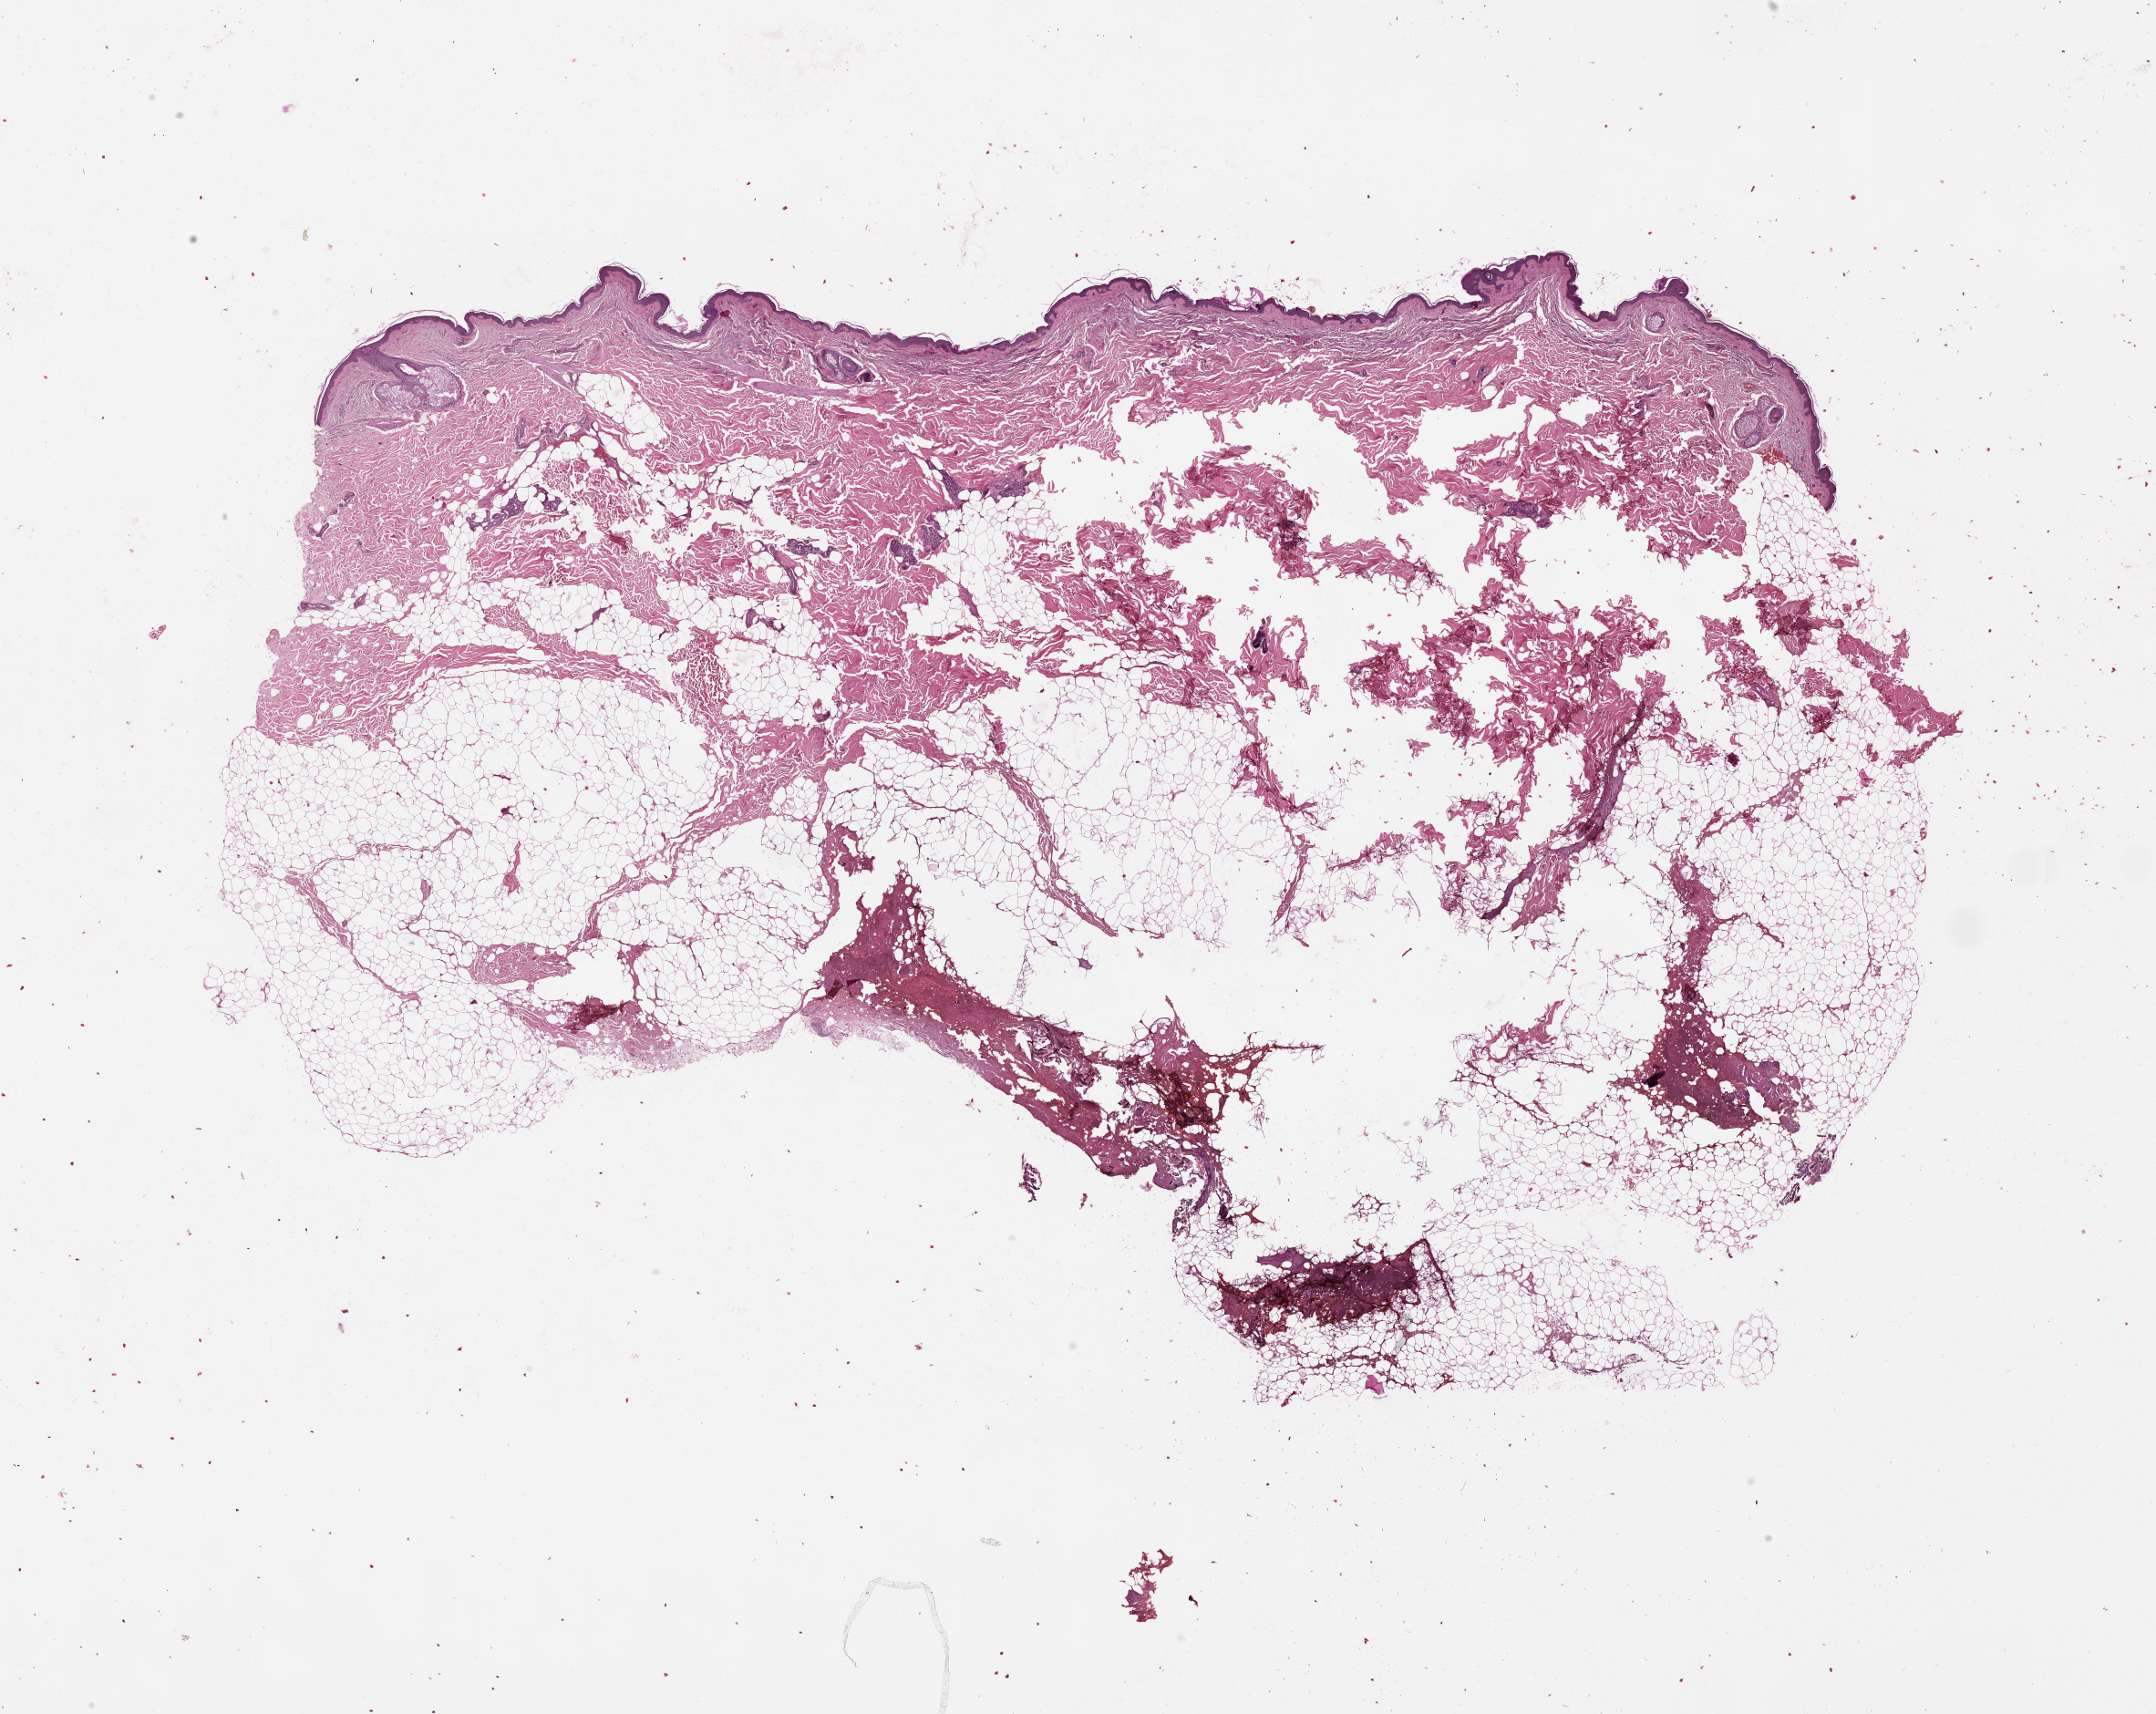
Whole-slide histology image, H&E-stained, shown as a low-resolution overview of the whole scanned area (about 19.0 x 15.1 mm). Female, 68 y/o.
Patient diagnosis: Malignant melanoma, NOS.